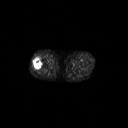
FDG PET of an extremity soft-tissue mass (from a PET/CT study), one axial slice. Position 236 of 267 along the scan axis. 128 × 128 image matrix, field of view 700 × 700 mm. Male patient, age 43 years. Case-level facts recorded for this patient, not image findings: histological type: poorly differentiated synovial sarcoma; grade: high; site of the primary tumour: right buttock.
Outlined on this slice (expert contour drawn on MRI and transferred to this co-registered scan by the dataset authors):
- gross tumour volume including surrounding oedema: bounding box (x1, y1, x2, y2) in pixels: (32, 57, 42, 70)
- gross tumour volume (mass): (33, 58, 42, 70)